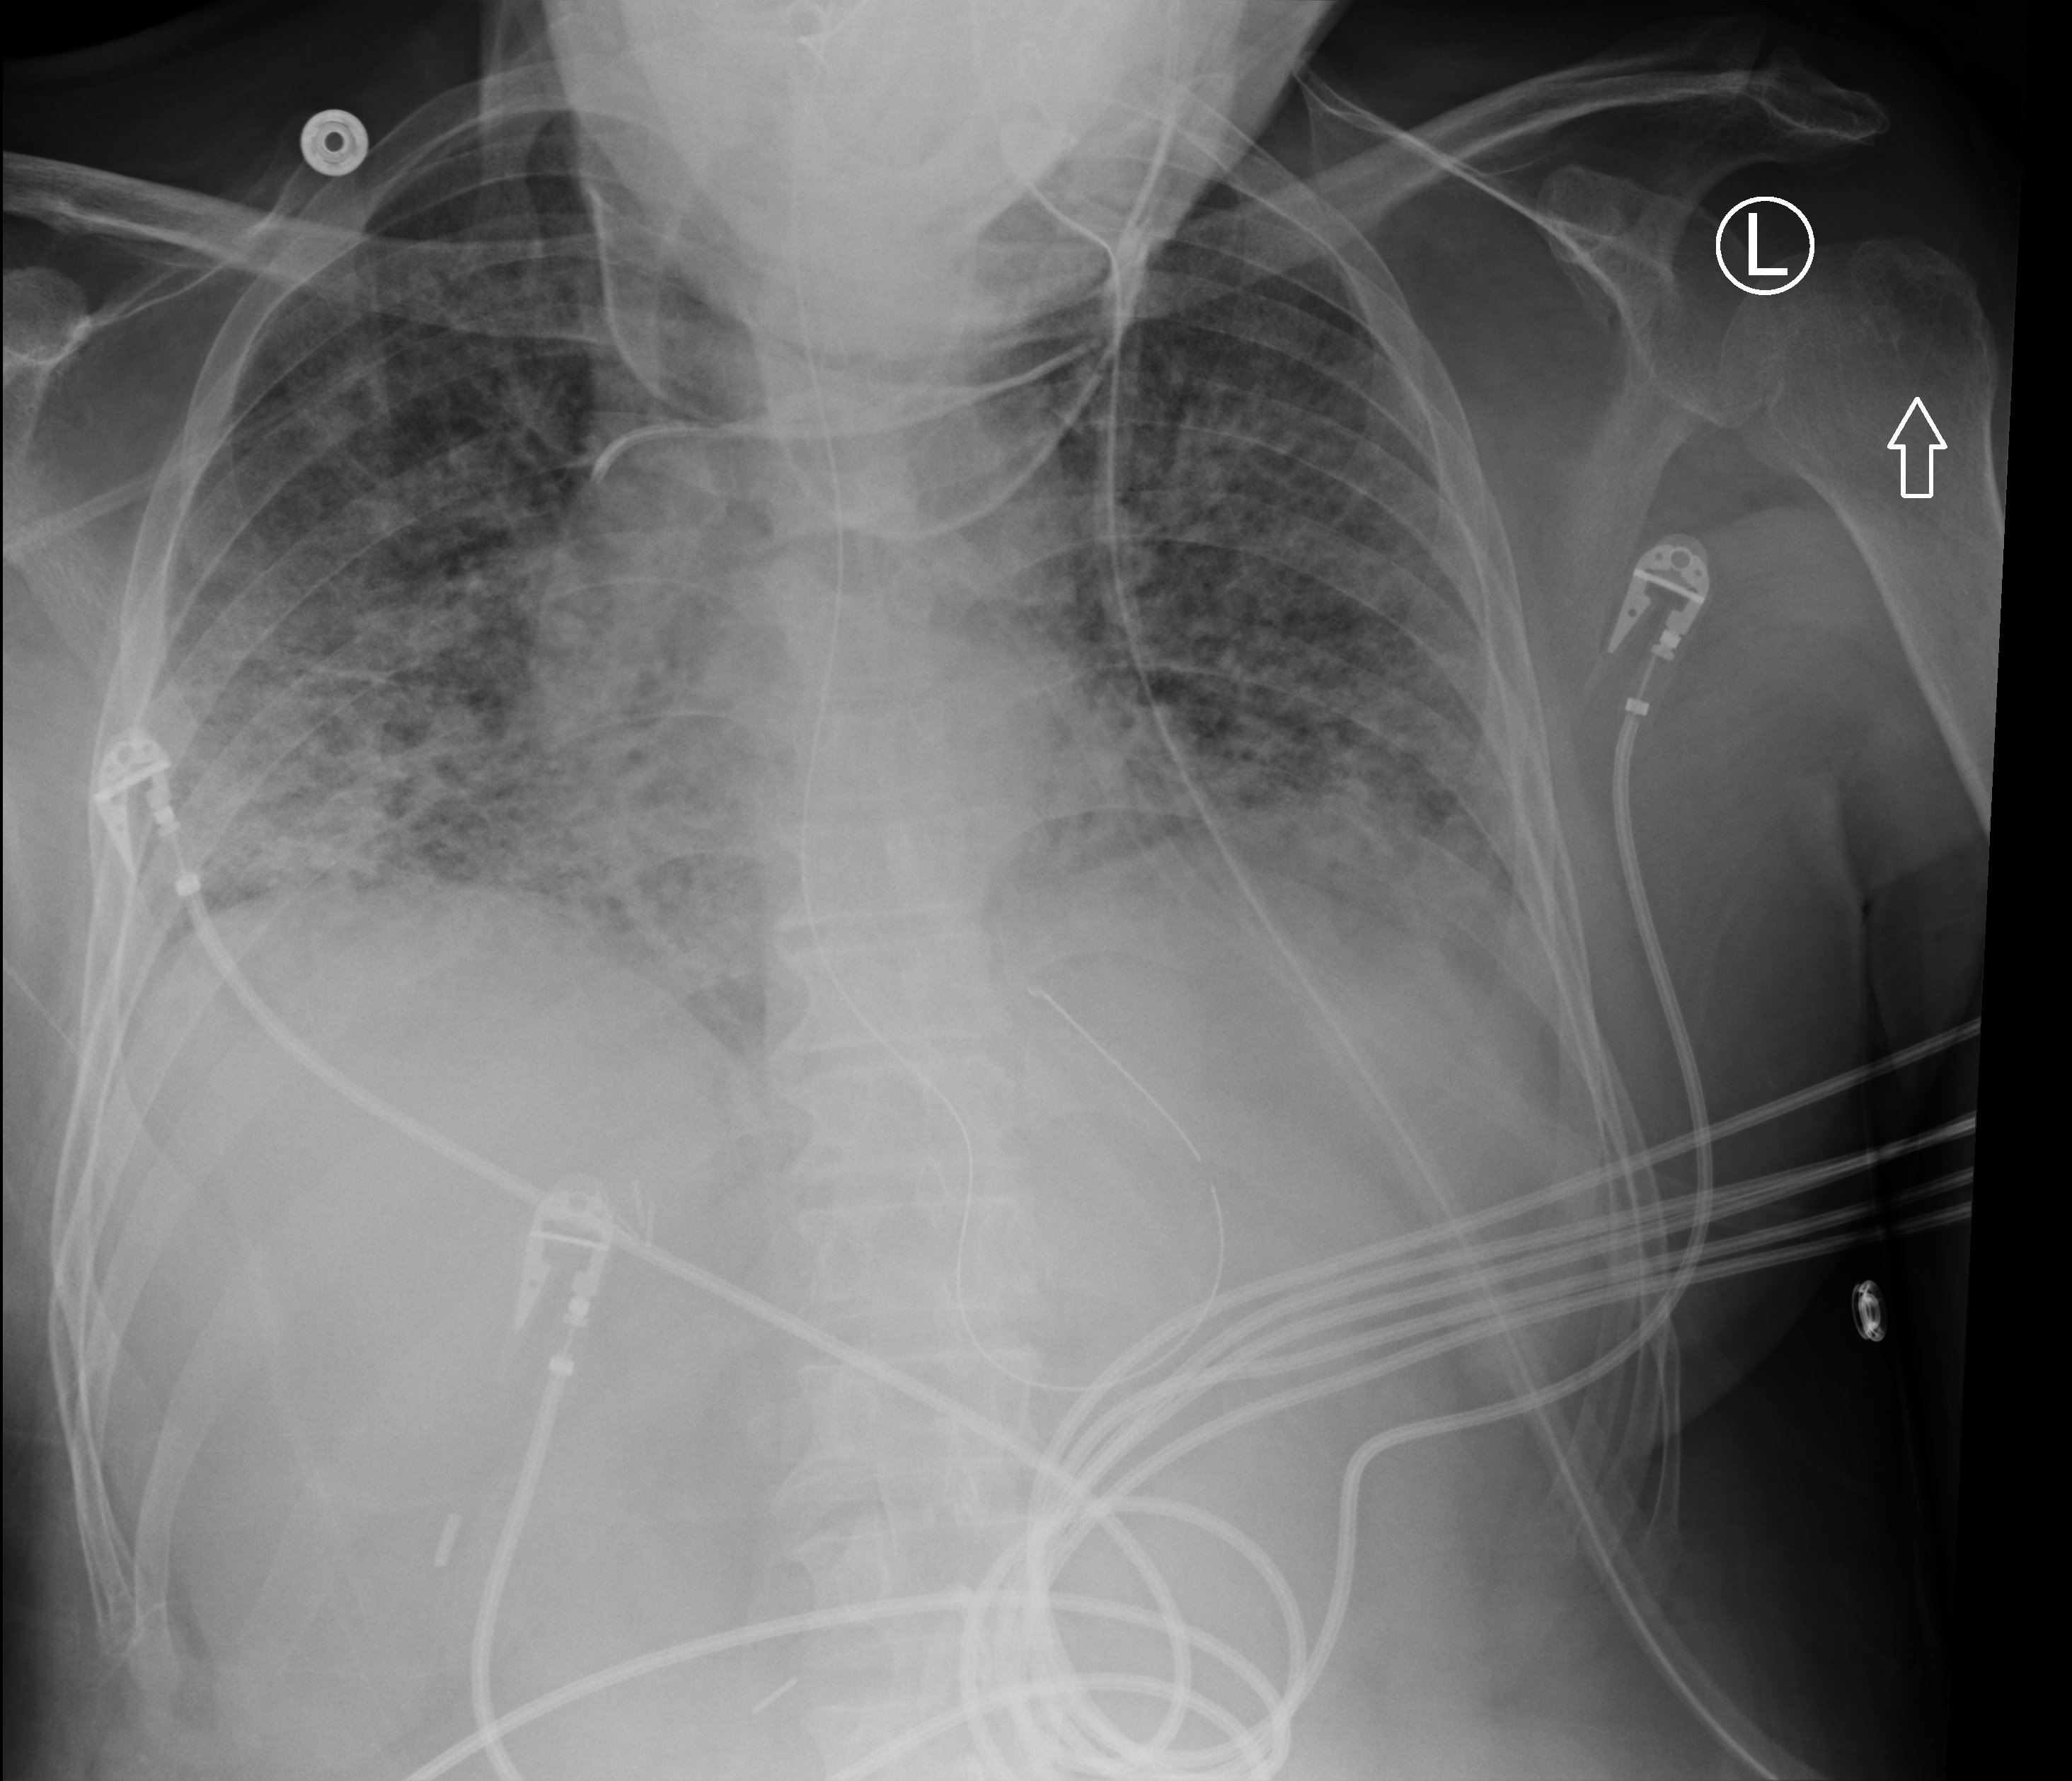
Bedside chest radiograph (computed radiography), anteroposterior (AP) projection. Patient hospitalised with COVID-19; male, aged 60–74 years.
Admission-level facts for this patient (not findings on this image; timing relative to this image not recorded): smoking status (admission record): never; admitted to intensive care during this hospital stay: yes.